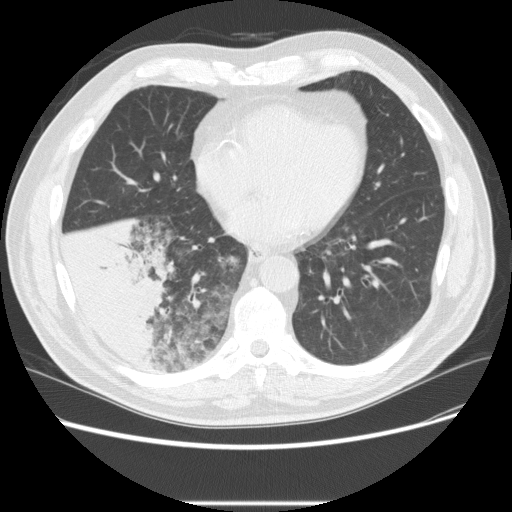
Low-dose screening chest CT, one axial slice. Position 88 of 233 along the scan axis. Reconstruction kernel STANDARD. 120 kVp. Lung window (W 1500 / L -600 HU). 512 × 512 image matrix, field of view 380 × 380 mm.
Annotated regions visible in this slice (manually delineated by an expert):
- lesion 3 (tumor, lower lobe of right lung): box from (x=59, y=215) to (x=177, y=363) px